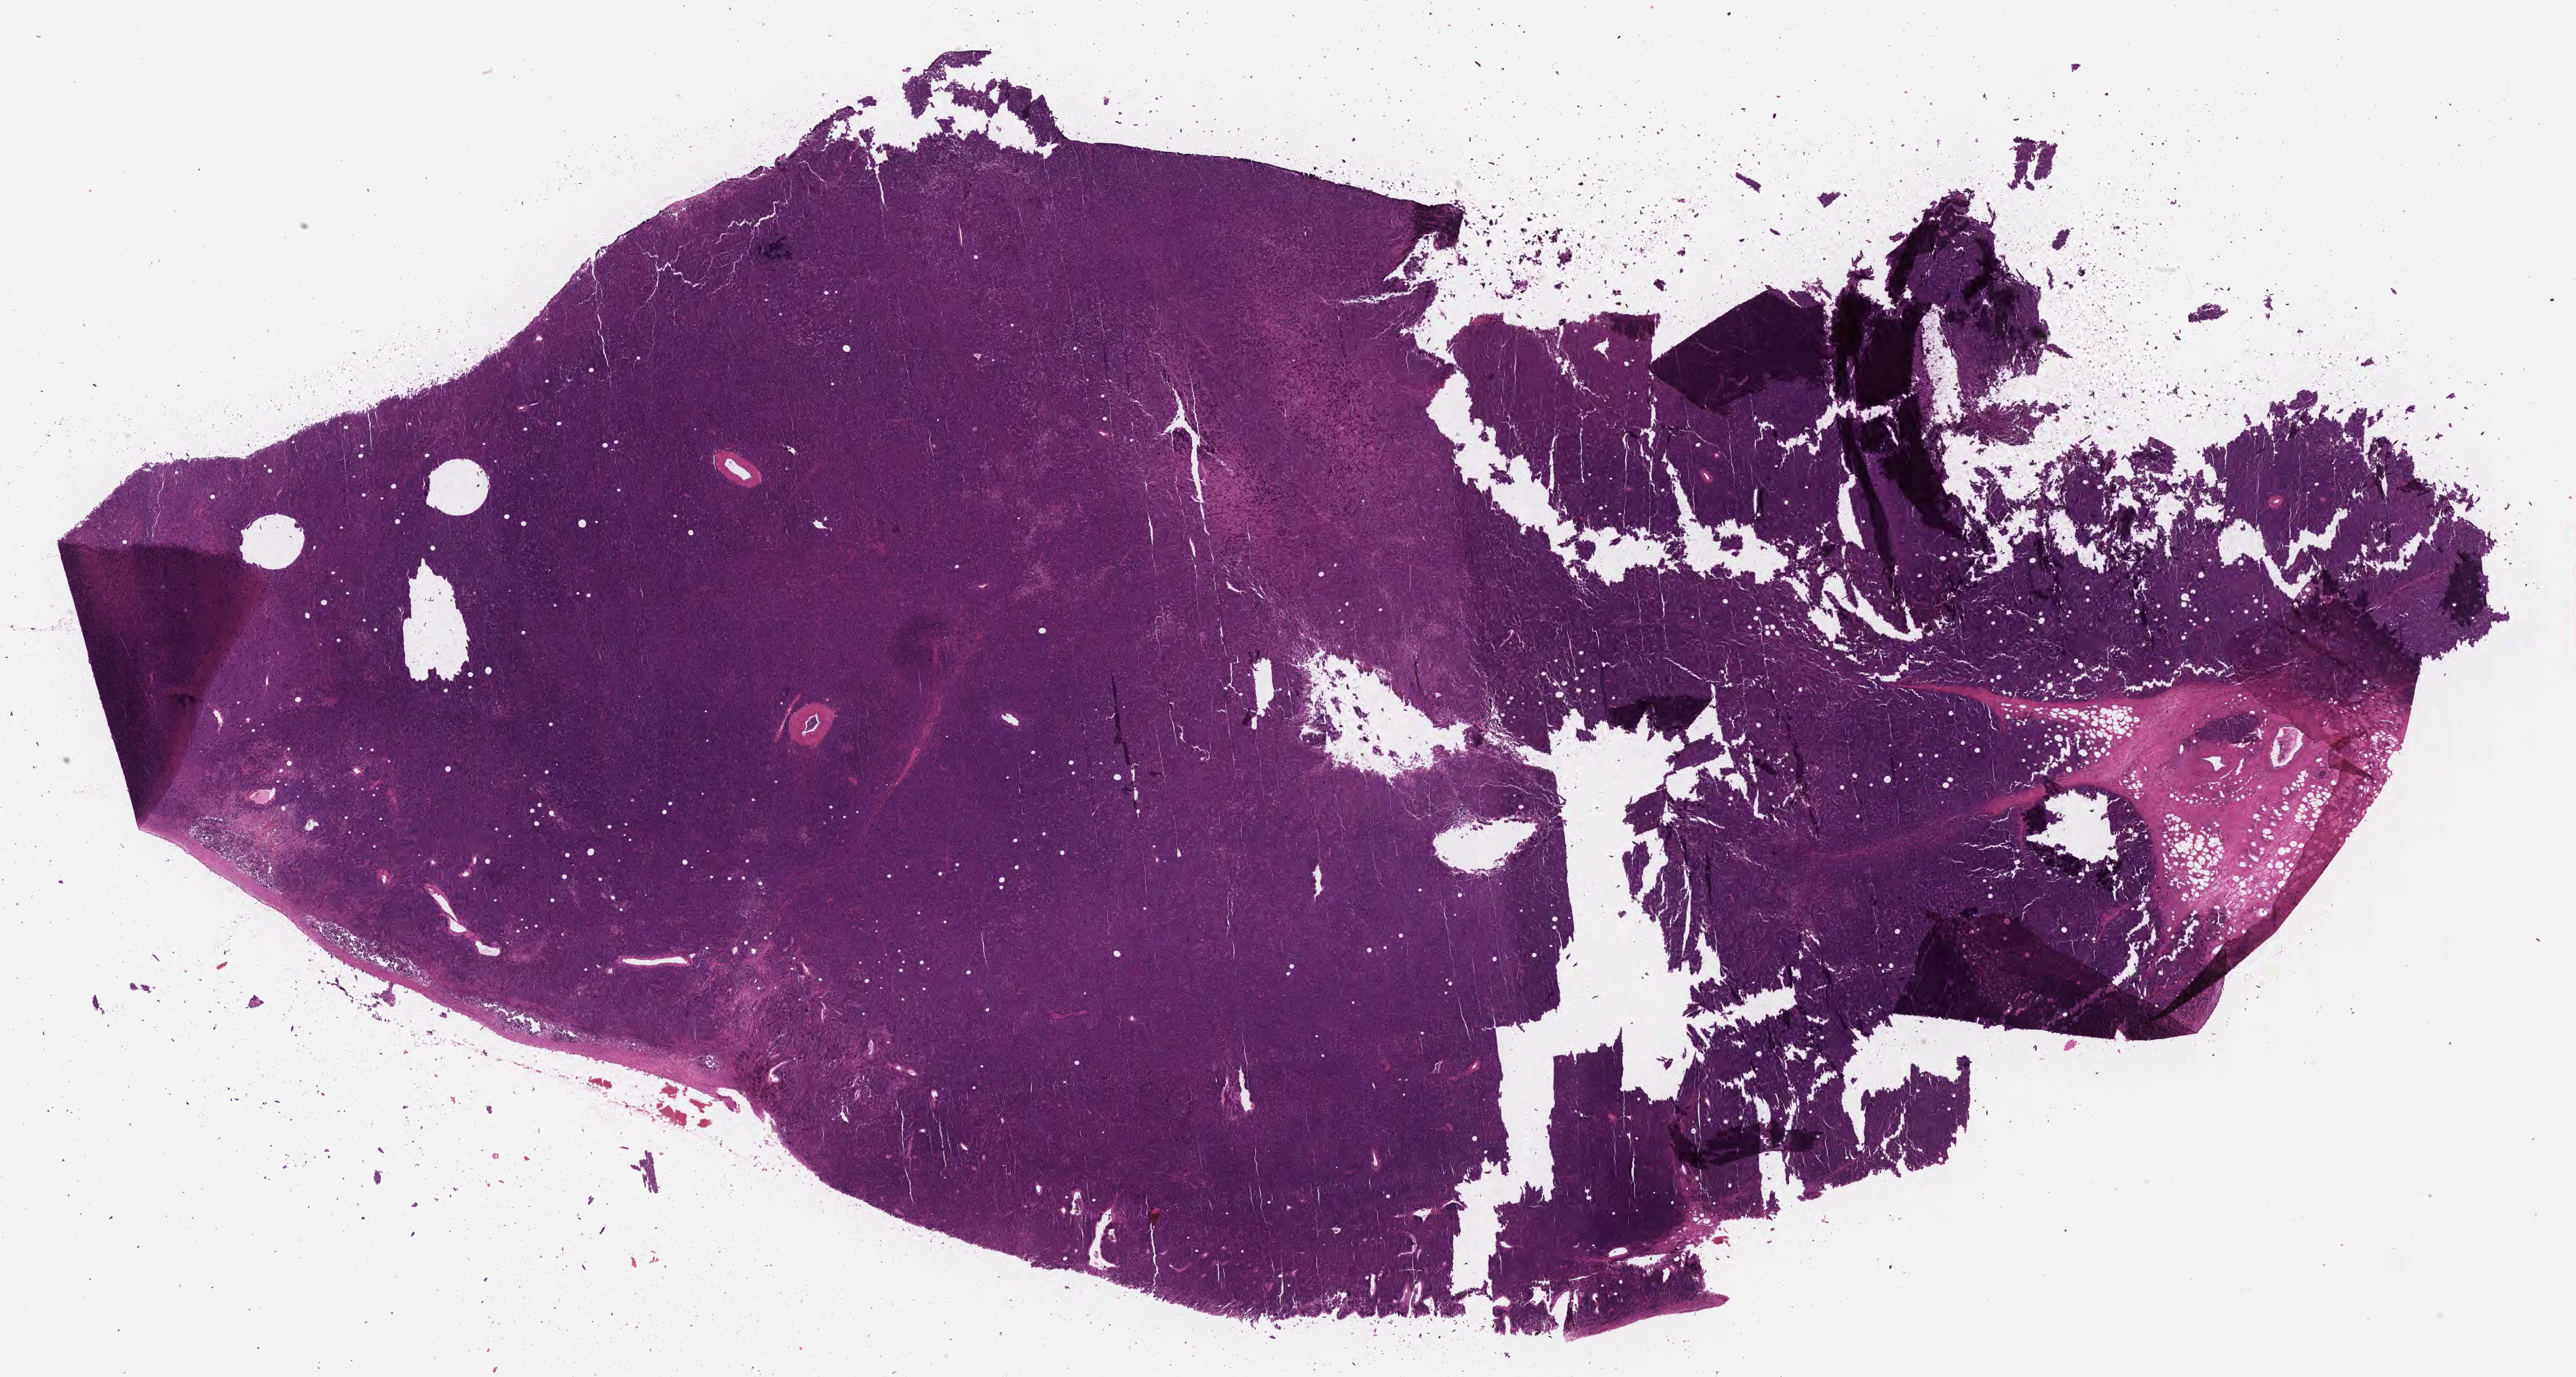
Hematoxylin and eosin (H&E) whole-slide image — whole scanned area (about 30.7 x 16.4 mm) shown as a low-resolution overview, formalin-fixed paraffin-embedded section, specimen: primary tumor. Patient: male, aged 51. Composition of this section per pathologist review: tumor cells 90%, tumor nuclei 95%, stromal cells 5%, necrosis 5%, normal cells 0%. Infiltration values recorded for this section: lymphocyte infiltration 40%, monocyte infiltration 35%, neutrophil infiltration 5%.
- histologic diagnosis: Burkitt lymphoma, NOS
- Ann Arbor stage (patient): Stage IV